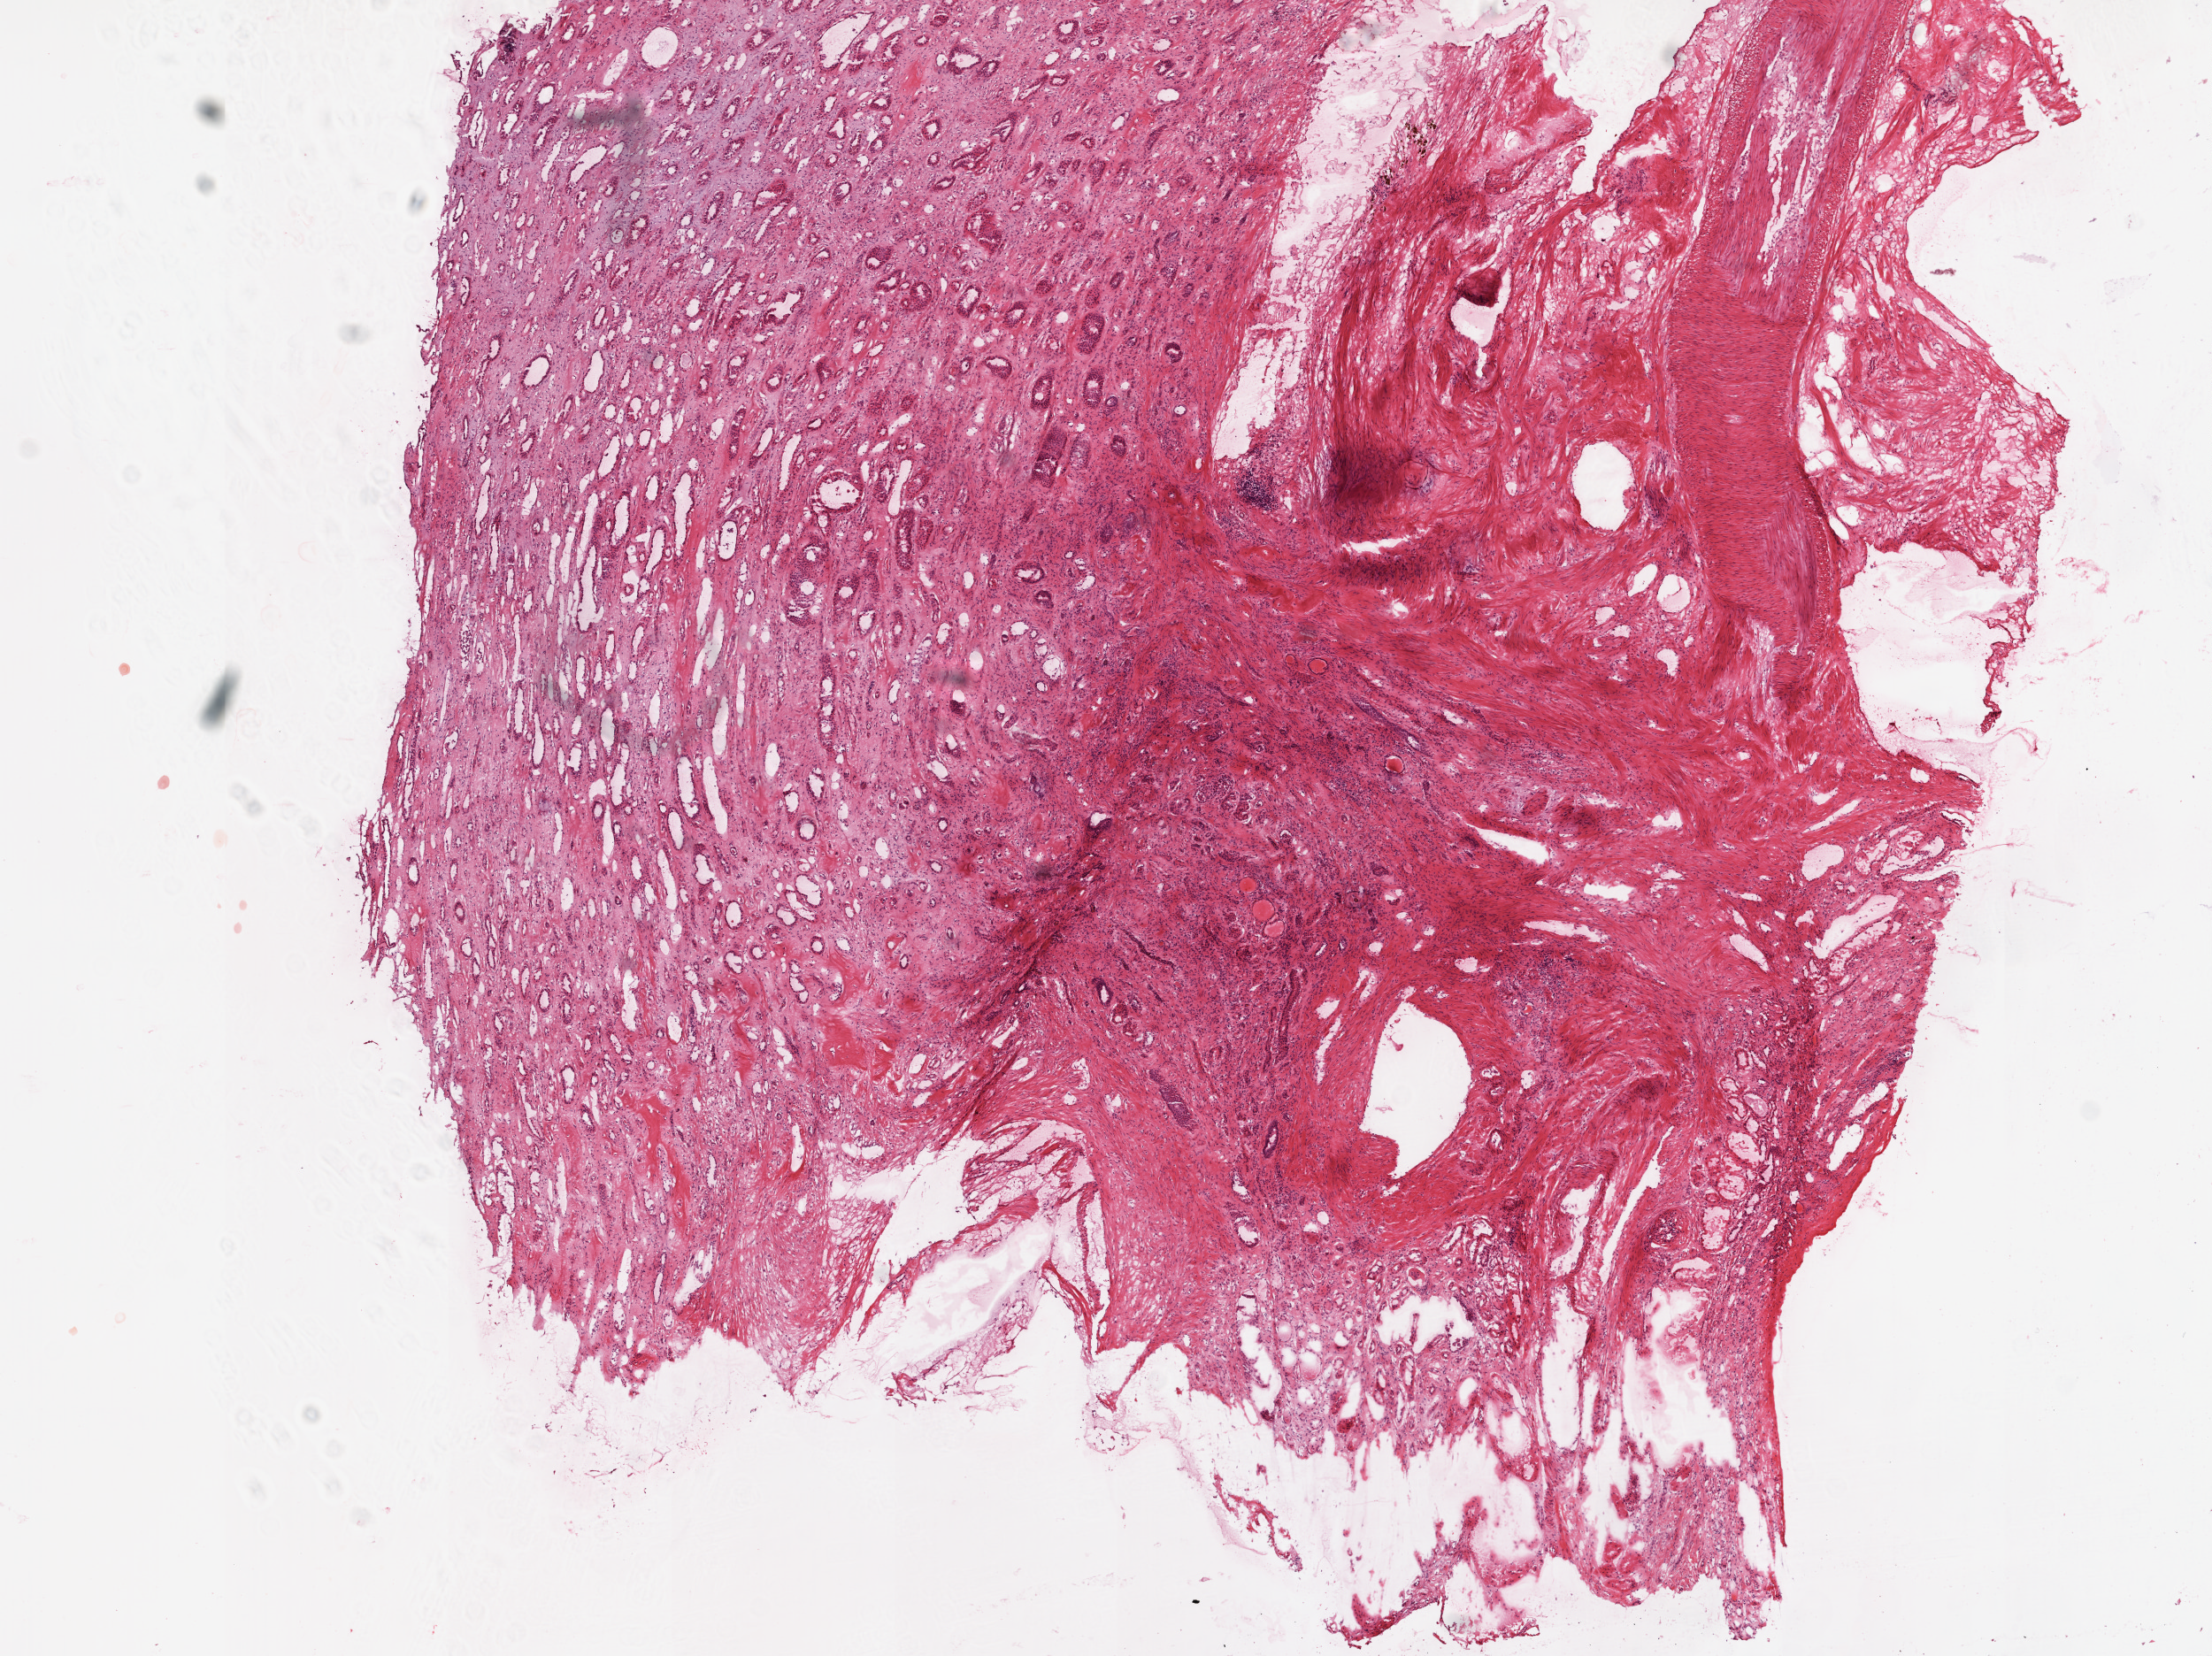
Digitized H&E tissue section (whole slide), whole scanned area (about 10.0 x 7.5 mm, from a 20x scan) shown as a low-resolution overview, frozen section from the top of the tissue portion, solid tissue normal (non-tumour tissue) sample from the kidney. Patient: male, age at initial diagnosis 81 years.
• this section: solid tissue normal (non-tumour) sample from the same patient
• patient diagnosis: Clear cell adenocarcinoma, NOS